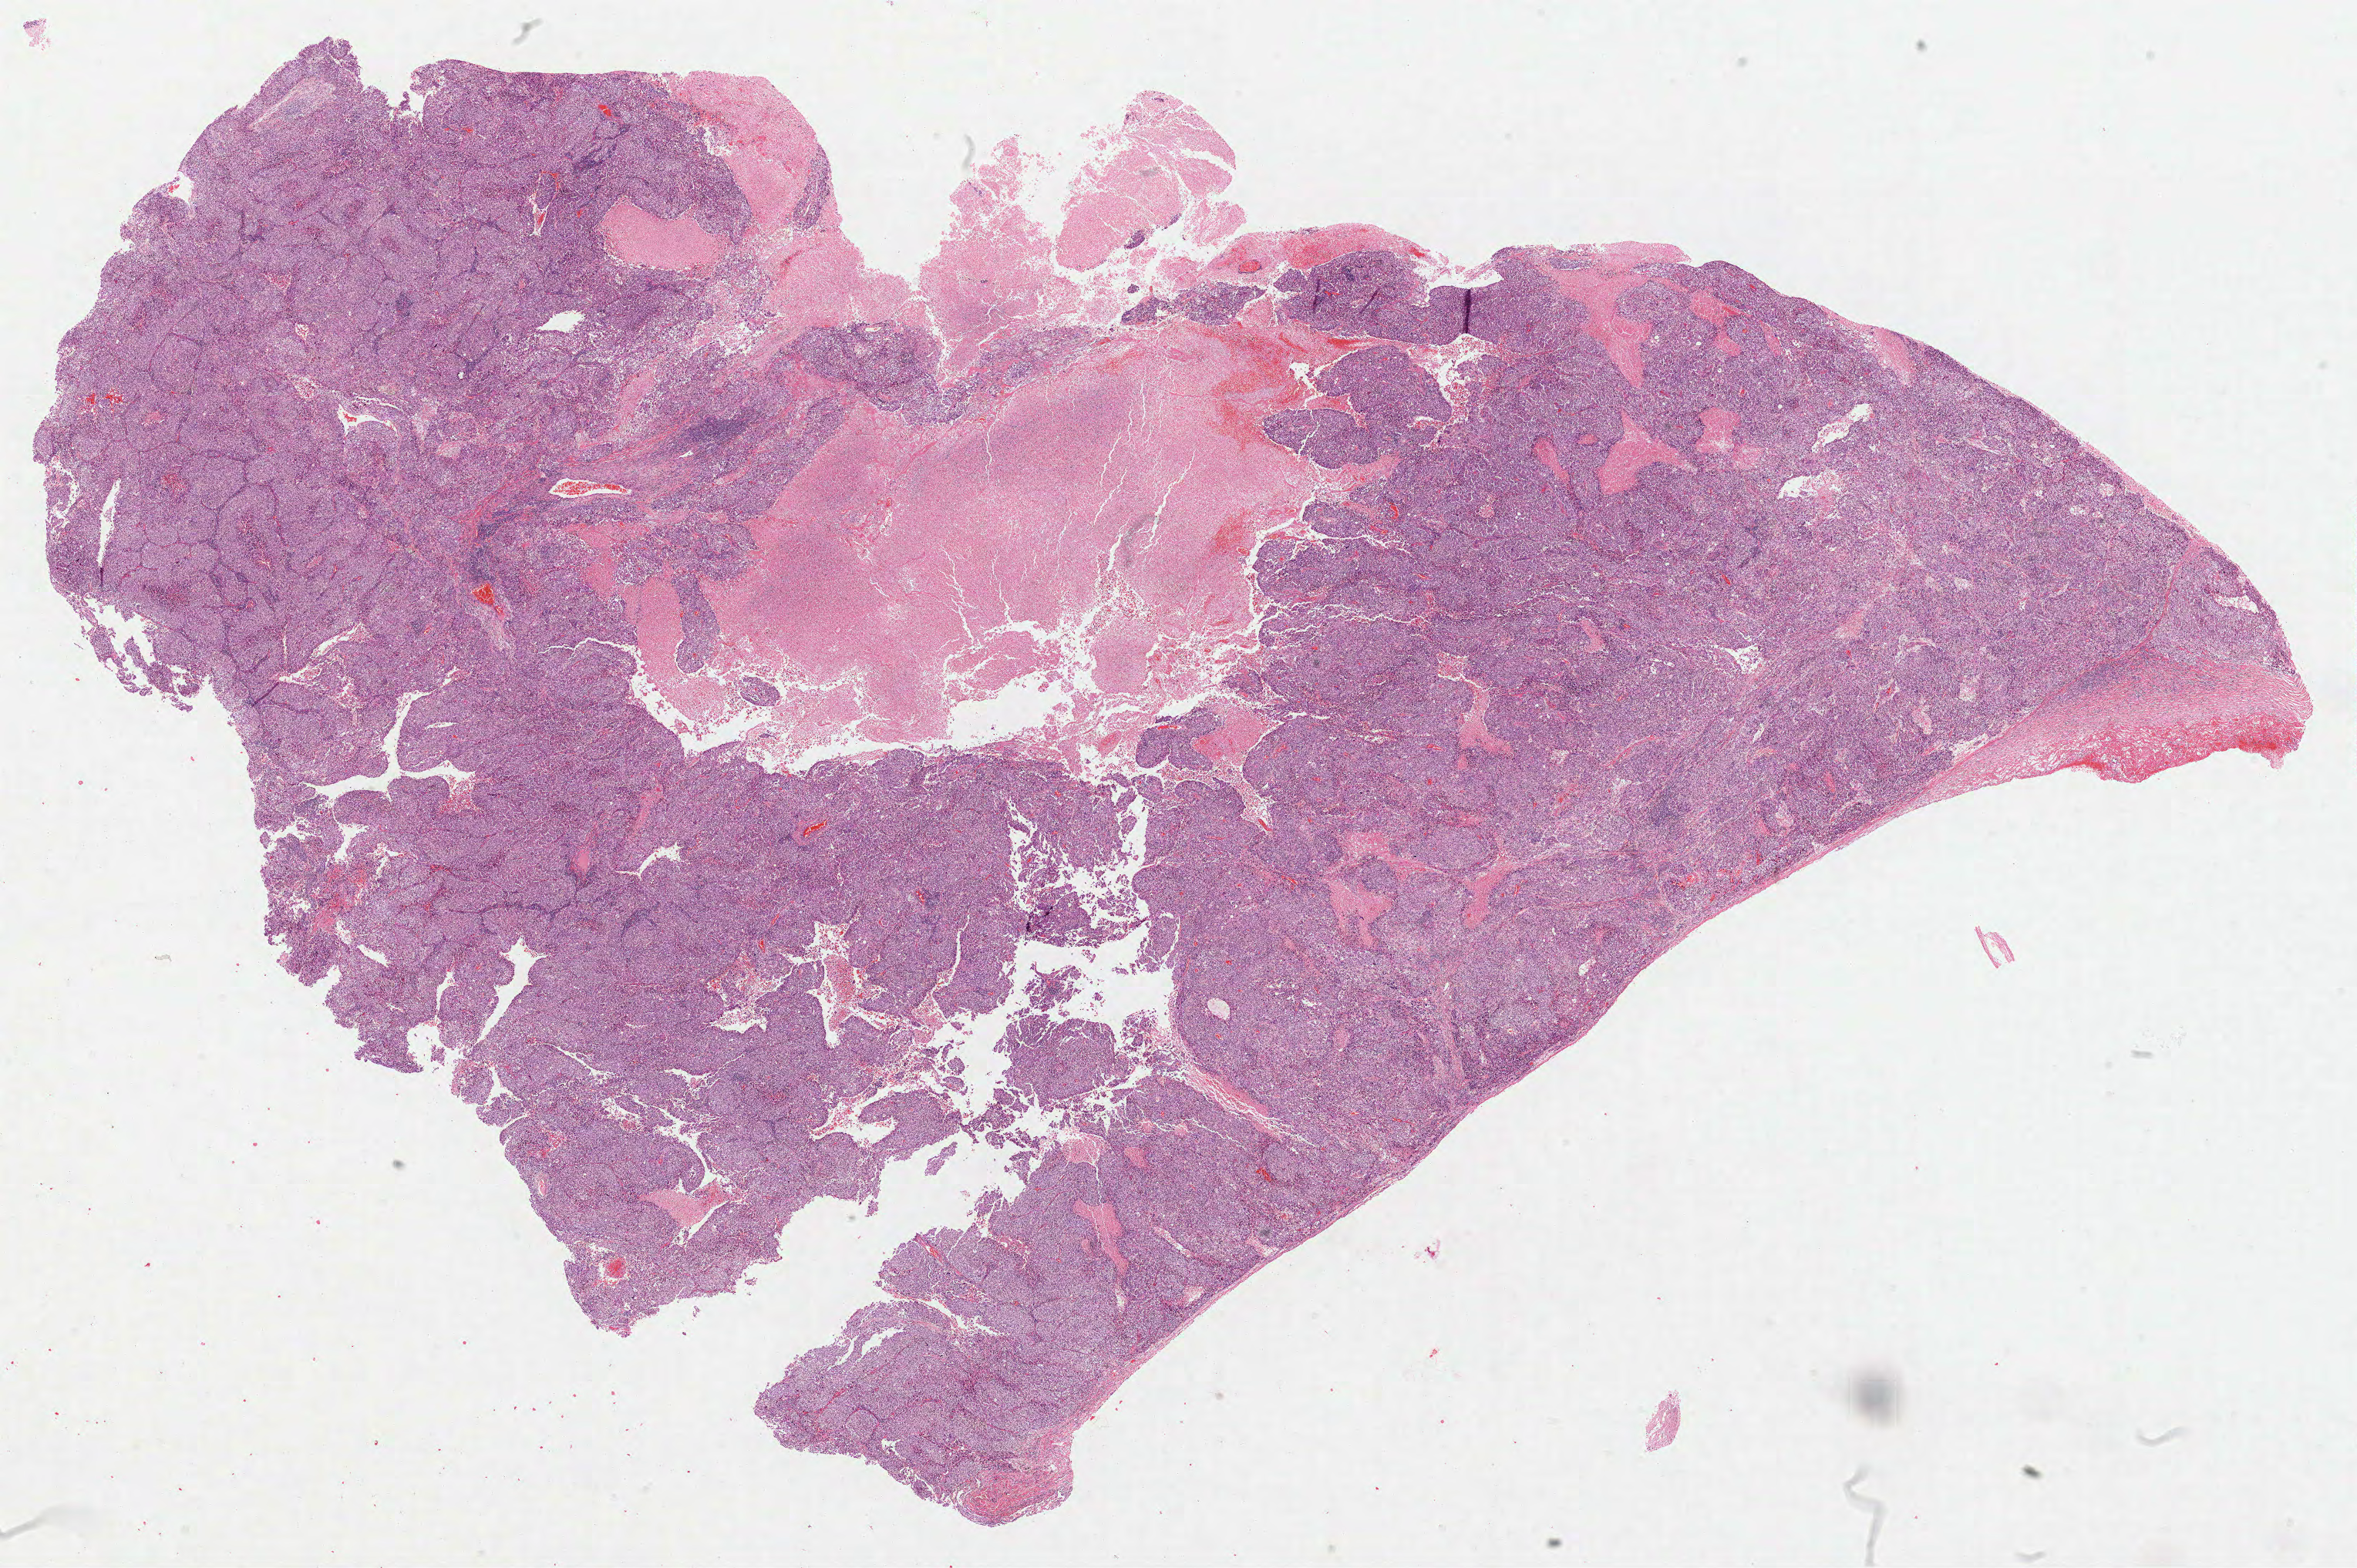
Whole-slide histology image, H&E — whole scanned area (about 24.7 x 16.4 mm) shown as a low-resolution overview. Formalin-fixed paraffin-embedded (FFPE) diagnostic section. Primary tumour sample from the lung. Patient: male, age at initial diagnosis 67 years.
Diagnosis: Squamous cell carcinoma, NOS (upper lobe, lung).